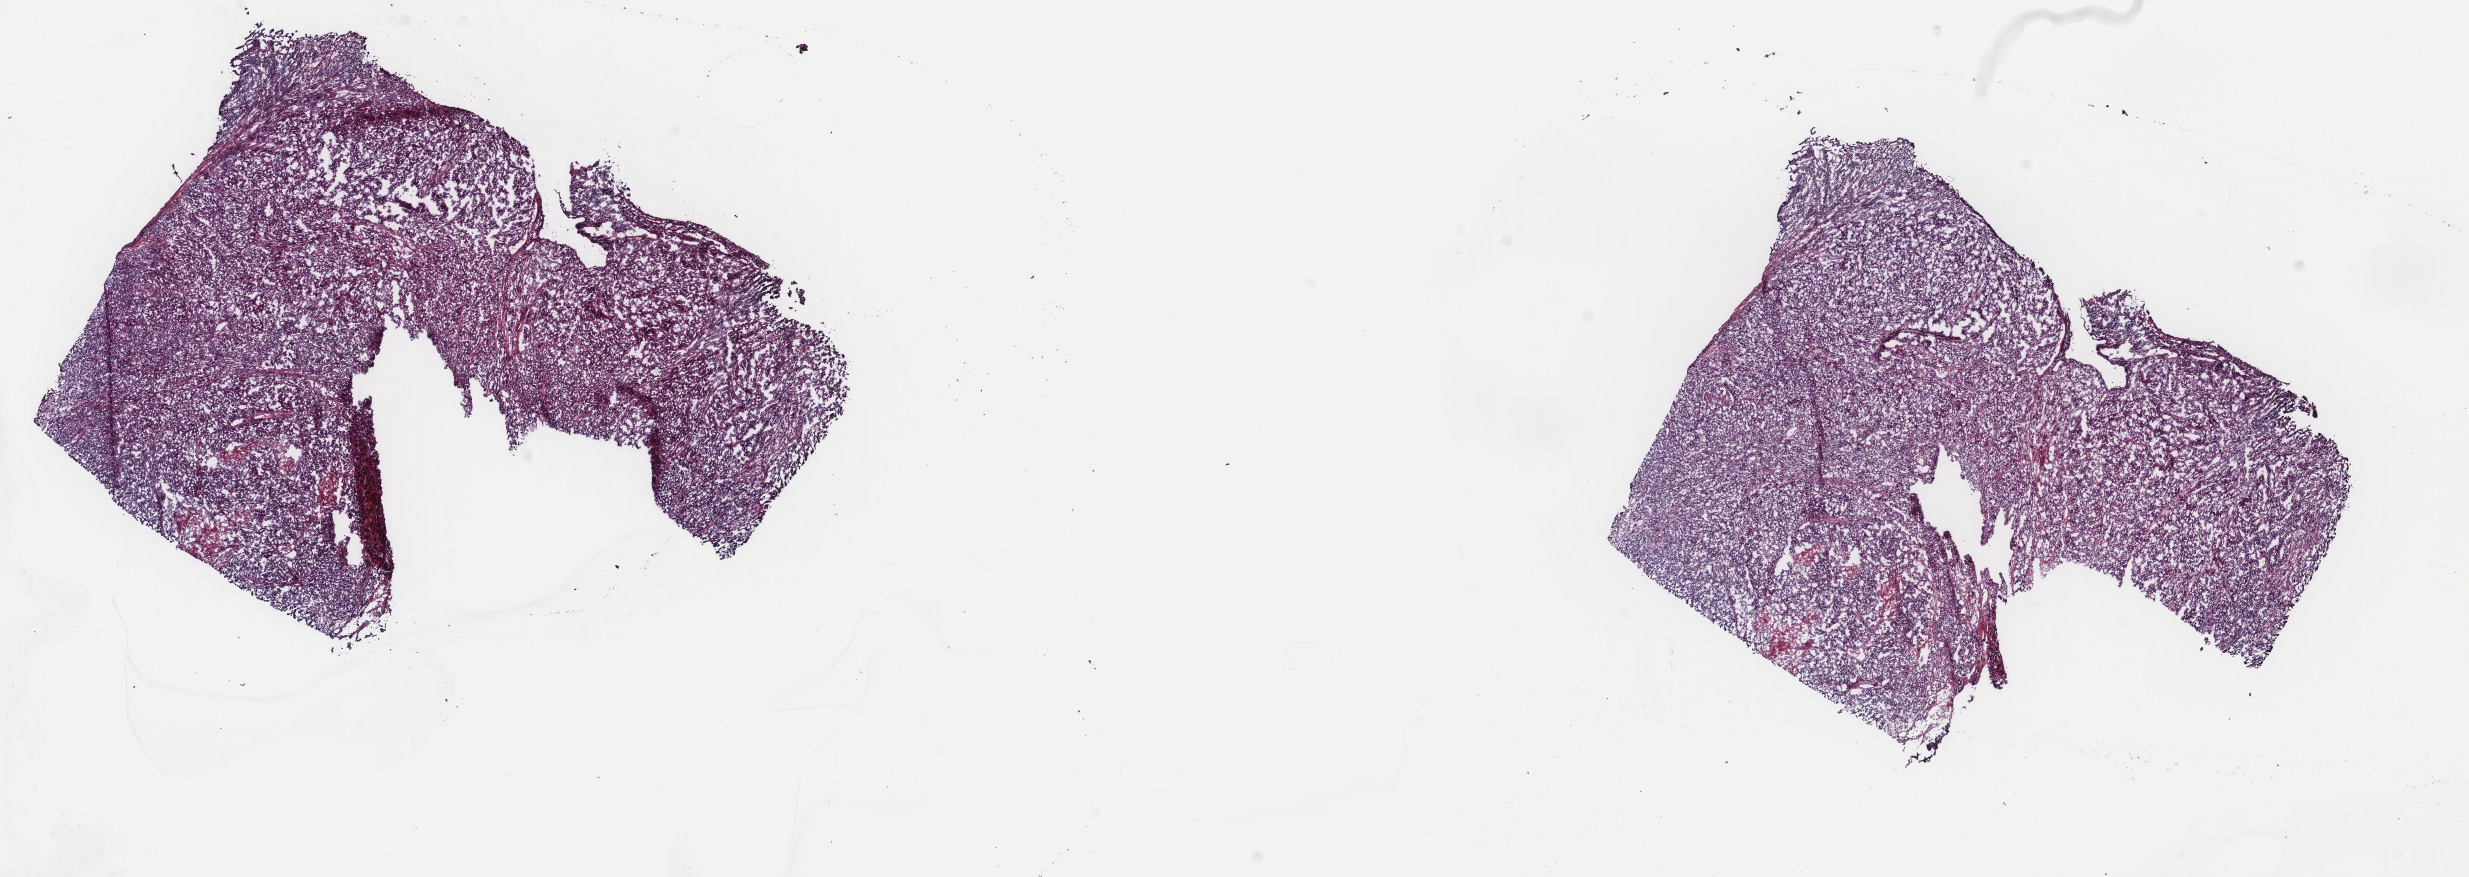
Hematoxylin and eosin (H&E) stained whole-slide image, a low-resolution overview of the entire scanned area, about 19.6 x 7.0 mm (from a 40x scan); frozen section; metastatic tumour sample, sampled site: lymph nodes of axilla or arm. Female patient; age at initial diagnosis 59 years.
This section: metastatic tumour tissue. Patient diagnosis: Malignant melanoma, NOS.